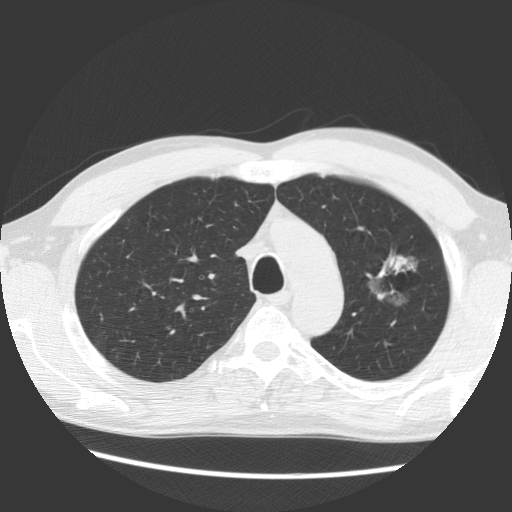
Chest CT (low-dose screening protocol), one axial image. First (baseline) screen. Lung window (W 1500 / L -600 HU). 2.5 mm slice thickness. Standard (soft-tissue) reconstruction kernel (STANDARD). 140 kVp. Slice 103 of 138 in the series. 512 × 512 image matrix. Male participant, aged 61 years at enrolment. Former smoker at enrolment.
• Expert reader's lesion annotation, box from (x=353, y=241) to (x=438, y=319) px.
• The exam's reader record, not a measurement of the box and not confirmed to be the same lesion: non-calcified nodule or mass ≥4 mm, left upper lobe, 17 × 14 mm, soft tissue attenuation.
• Participant outcome: lung cancer diagnosed 1061 days after this screen — bronchiolo-alveolar adenocarcinoma, NOS, left upper lobe, well differentiated (G1), stage IB (AJCC 6th edition), 44 mm at pathology.